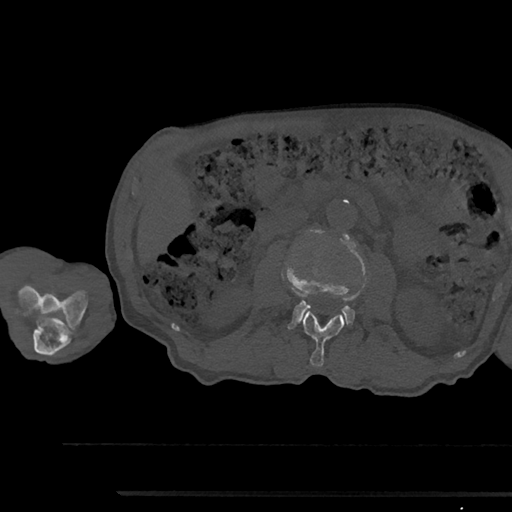
CT including the spine, one axial slice. Position 529 of 797 along the scan axis. Reconstruction kernel Br40s/3. 120 kVp. Bone window (W 1800 / L 400 HU). 0.5 mm slice thickness. 512 × 512 image matrix, field of view 367 × 367 mm. Patient: male, 79 years. Case-level facts recorded for this patient, not image findings: primary cancer: prostate.
Structures marked on this image (semi-automatically segmented with operator editing):
- L2 vertebra: box from (x=301, y=311) to (x=345, y=367) px
- L3 vertebra: (x=284, y=230)–(x=367, y=330)